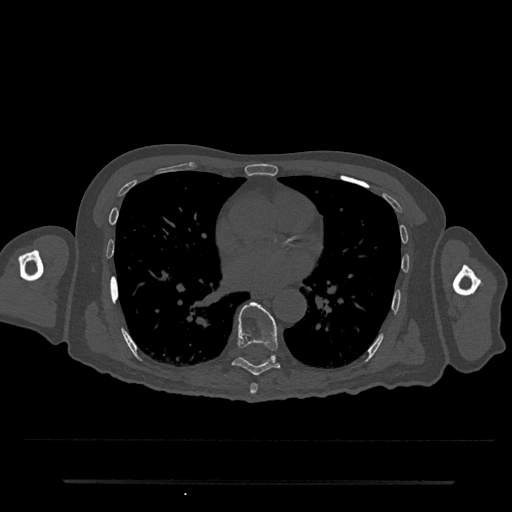
CT including the spine, one axial slice. Slice 419 of 797 in the series (ordered by position). Reconstruction kernel Br40s/3. 120 kVp. Bone window (W 1800 / L 400 HU). 512 × 512 image matrix, field of view 427 × 427 mm. Male patient, age 74 years. From the clinical record (not read from this slice): primary cancer: prostate.
Annotated regions visible in this slice (semi-automatic segmentation, software-assisted and operator-edited):
- T7 vertebra: bounding box (x1, y1, x2, y2) in pixels: (250, 383, 258, 394)
- T8 vertebra: (232, 302, 280, 376)